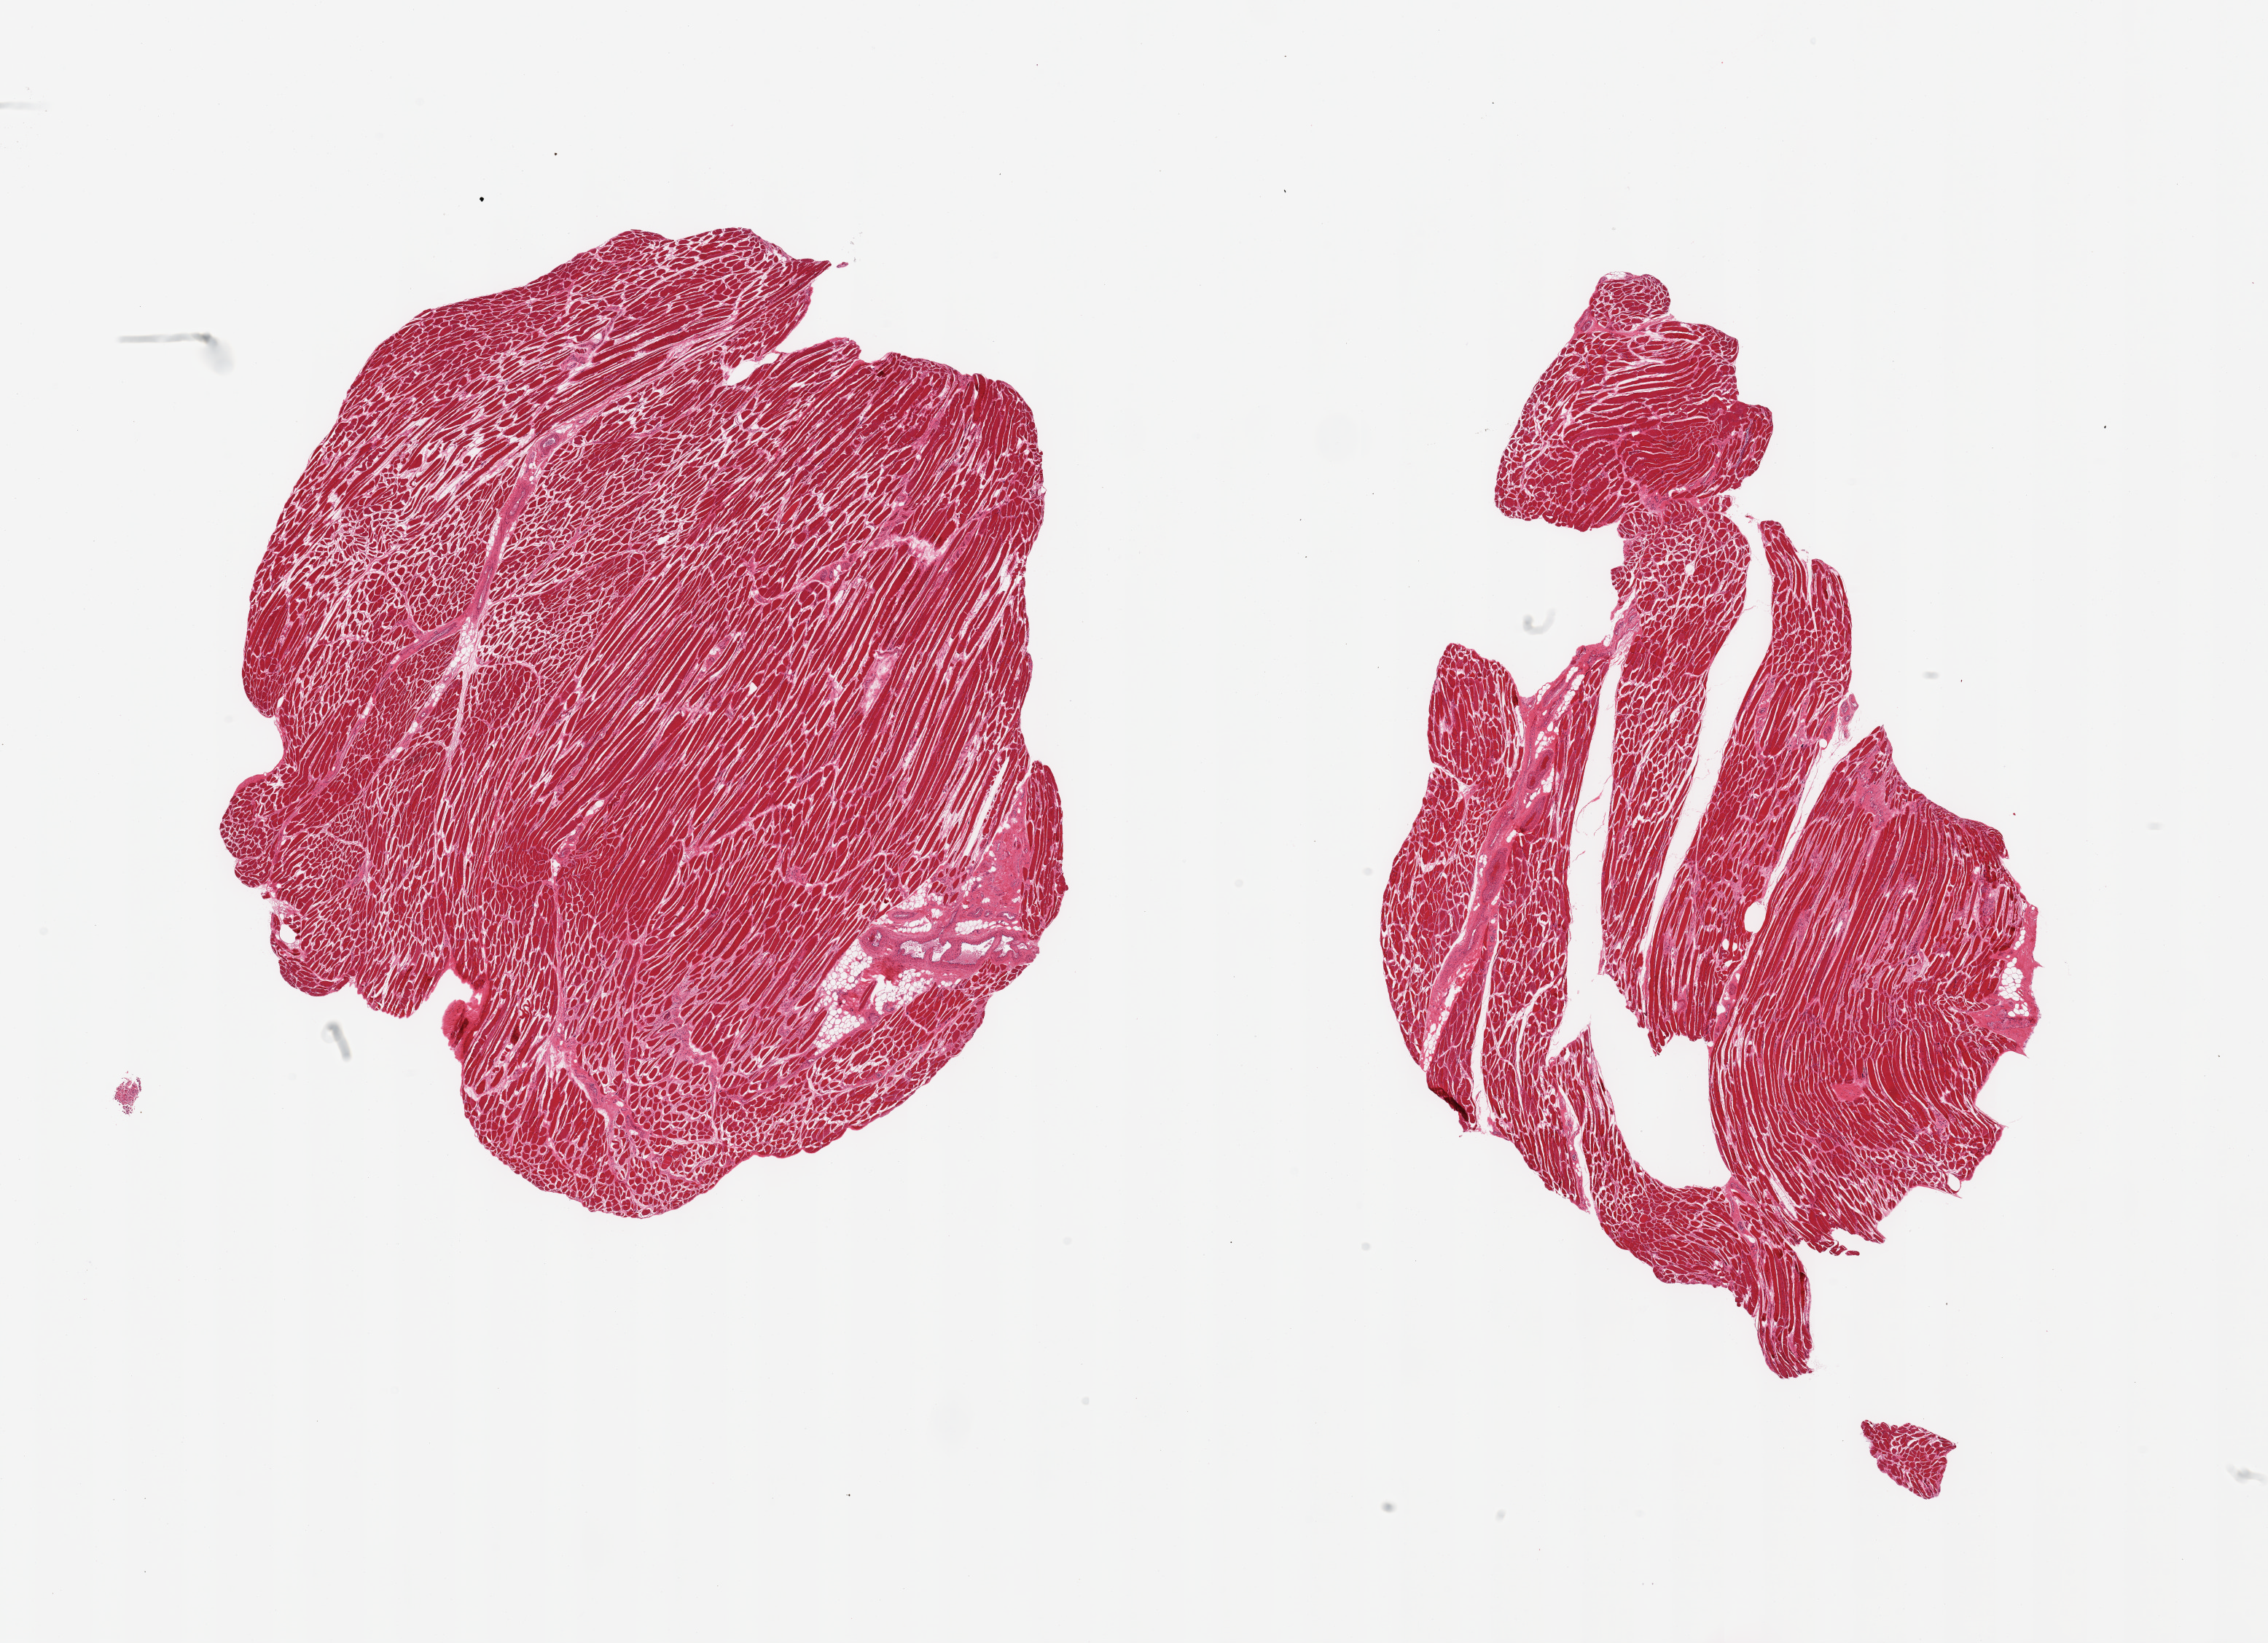
Digitized haematoxylin and eosin-stained section, brightfield — a low-resolution overview of the entire scanned area, about 24.6 x 17.8 mm (acquisition: 20x scan). PAXgene-fixed, paraffin-embedded tissue. Section of skeletal muscle (target tissue). Tissue donor sample.
Review note (as recorded): 2 pieces; rare atrophic fiber.